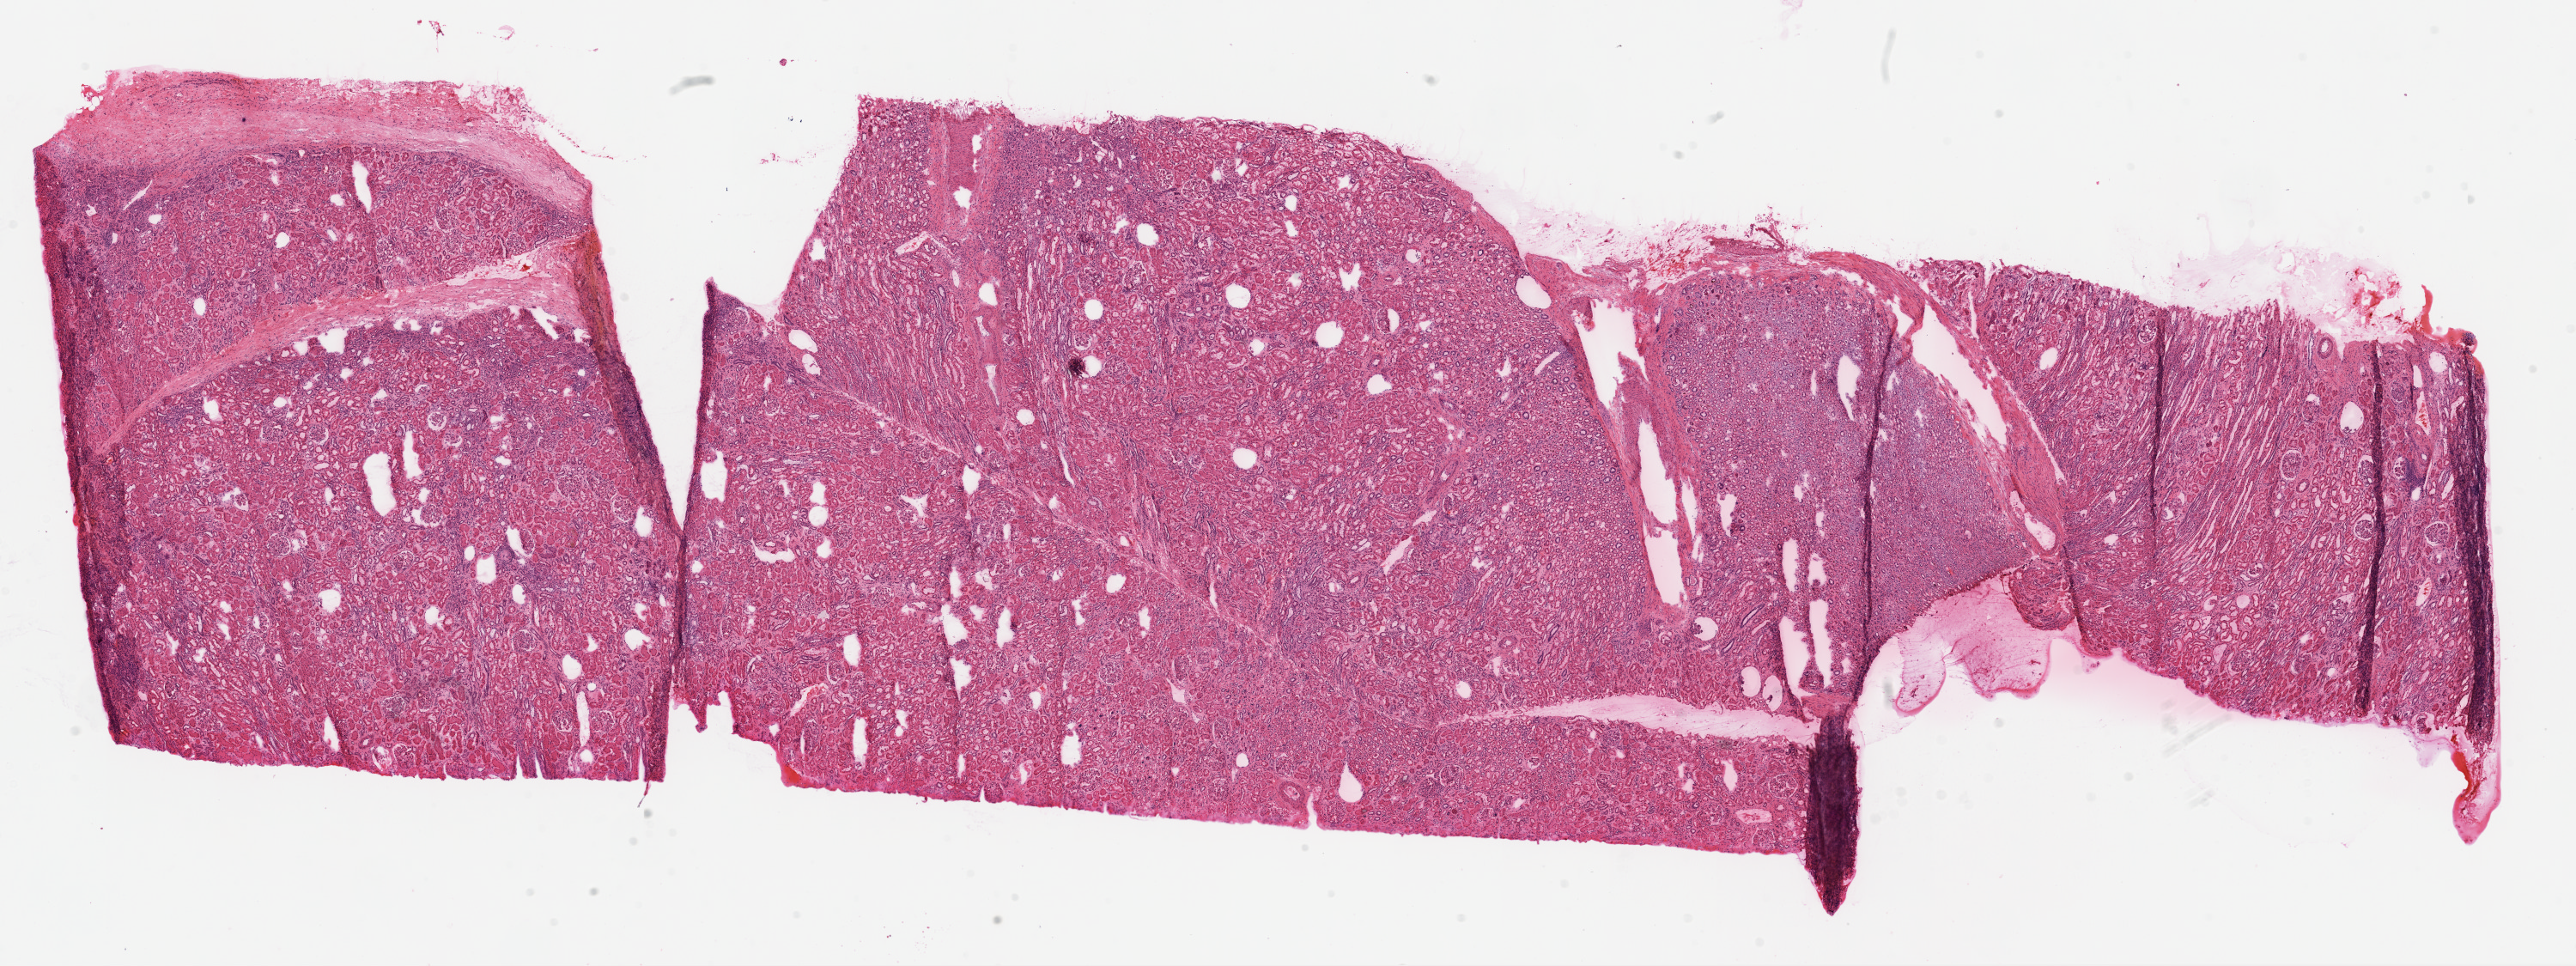
Hematoxylin and eosin (H&E) stained whole-slide image, low-resolution overview of the scanned area, about 24.1 x 9.0 mm (acquisition: 20x scan); frozen section from the top of the tissue portion; kidney, solid tissue normal (non-tumour tissue) sample. Male, age 47 years at initial diagnosis.
• this section: solid tissue normal sample (biorepository sample class)
• patient diagnosis: Clear cell adenocarcinoma, NOS